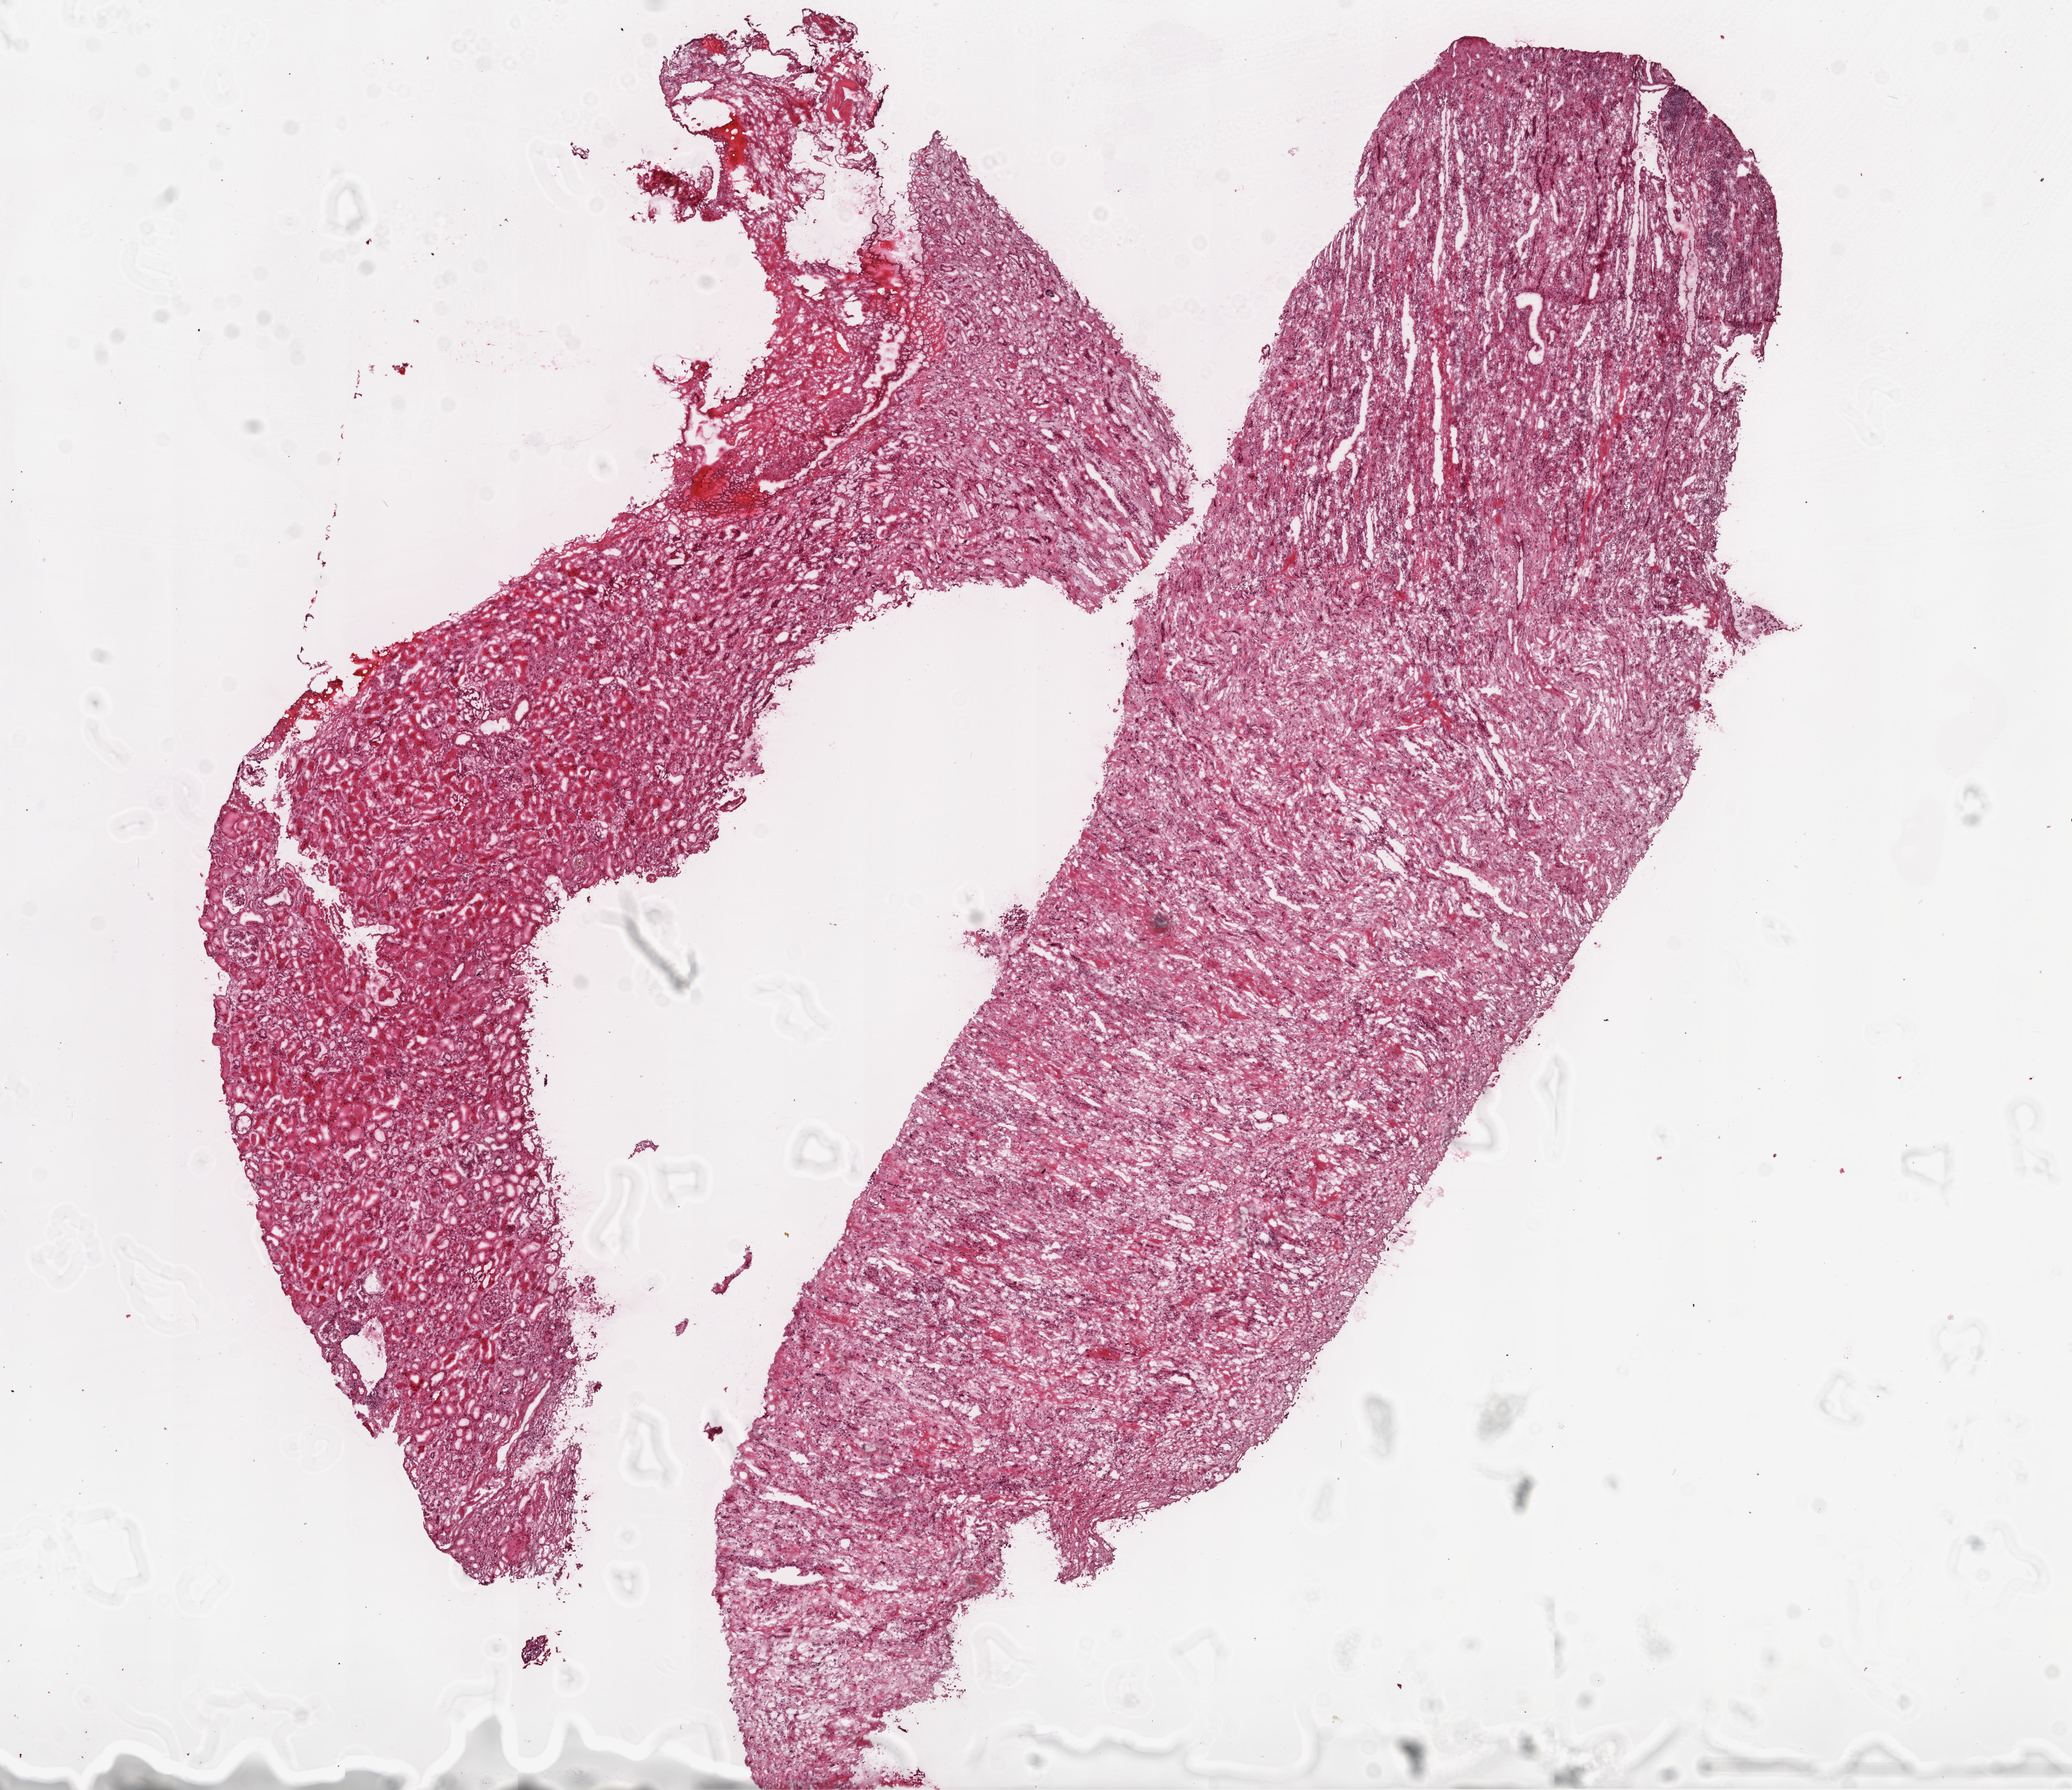
Whole-slide histology image, H&E — whole scanned area (about 12.0 x 10.4 mm) shown as a low-resolution overview; frozen section from the top of the tissue portion; sample: solid tissue normal (non-tumour tissue), kidney. Patient: male, age at initial diagnosis 79 years.
This section: solid tissue normal sample (biorepository sample class). Patient diagnosis: Clear cell adenocarcinoma, NOS.